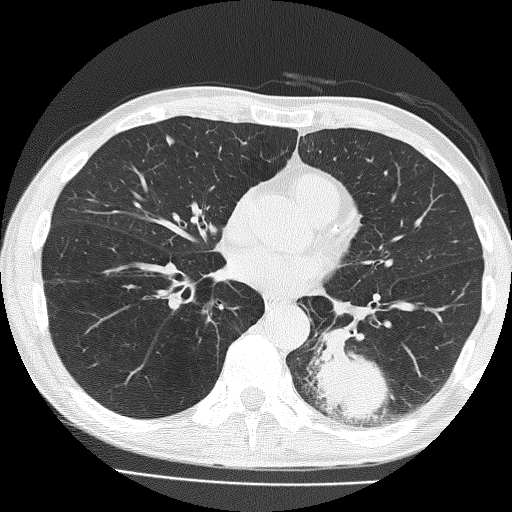
Chest CT (low-dose screening protocol), one axial image, first (baseline) screen, lung window (W 1500 / L -600 HU), lung (sharp) reconstruction kernel (FC51). Male participant, aged 58 years at enrolment. Current smoker at enrolment.
Lesion marked by an expert reader, bounding box <302,313,419,434> (left, top, right, bottom; pixels). The screening reader recorded 2 non-calcified nodules or masses ≥4 mm on this exam (left lower lobe, left upper lobe); which of them this box marks is not recorded. Later outcome: lung cancer diagnosed 39 days after this screen — non-small cell carcinoma, left lower lobe, poorly differentiated (G3), stage IV (AJCC 6th edition), 74 mm at pathology.